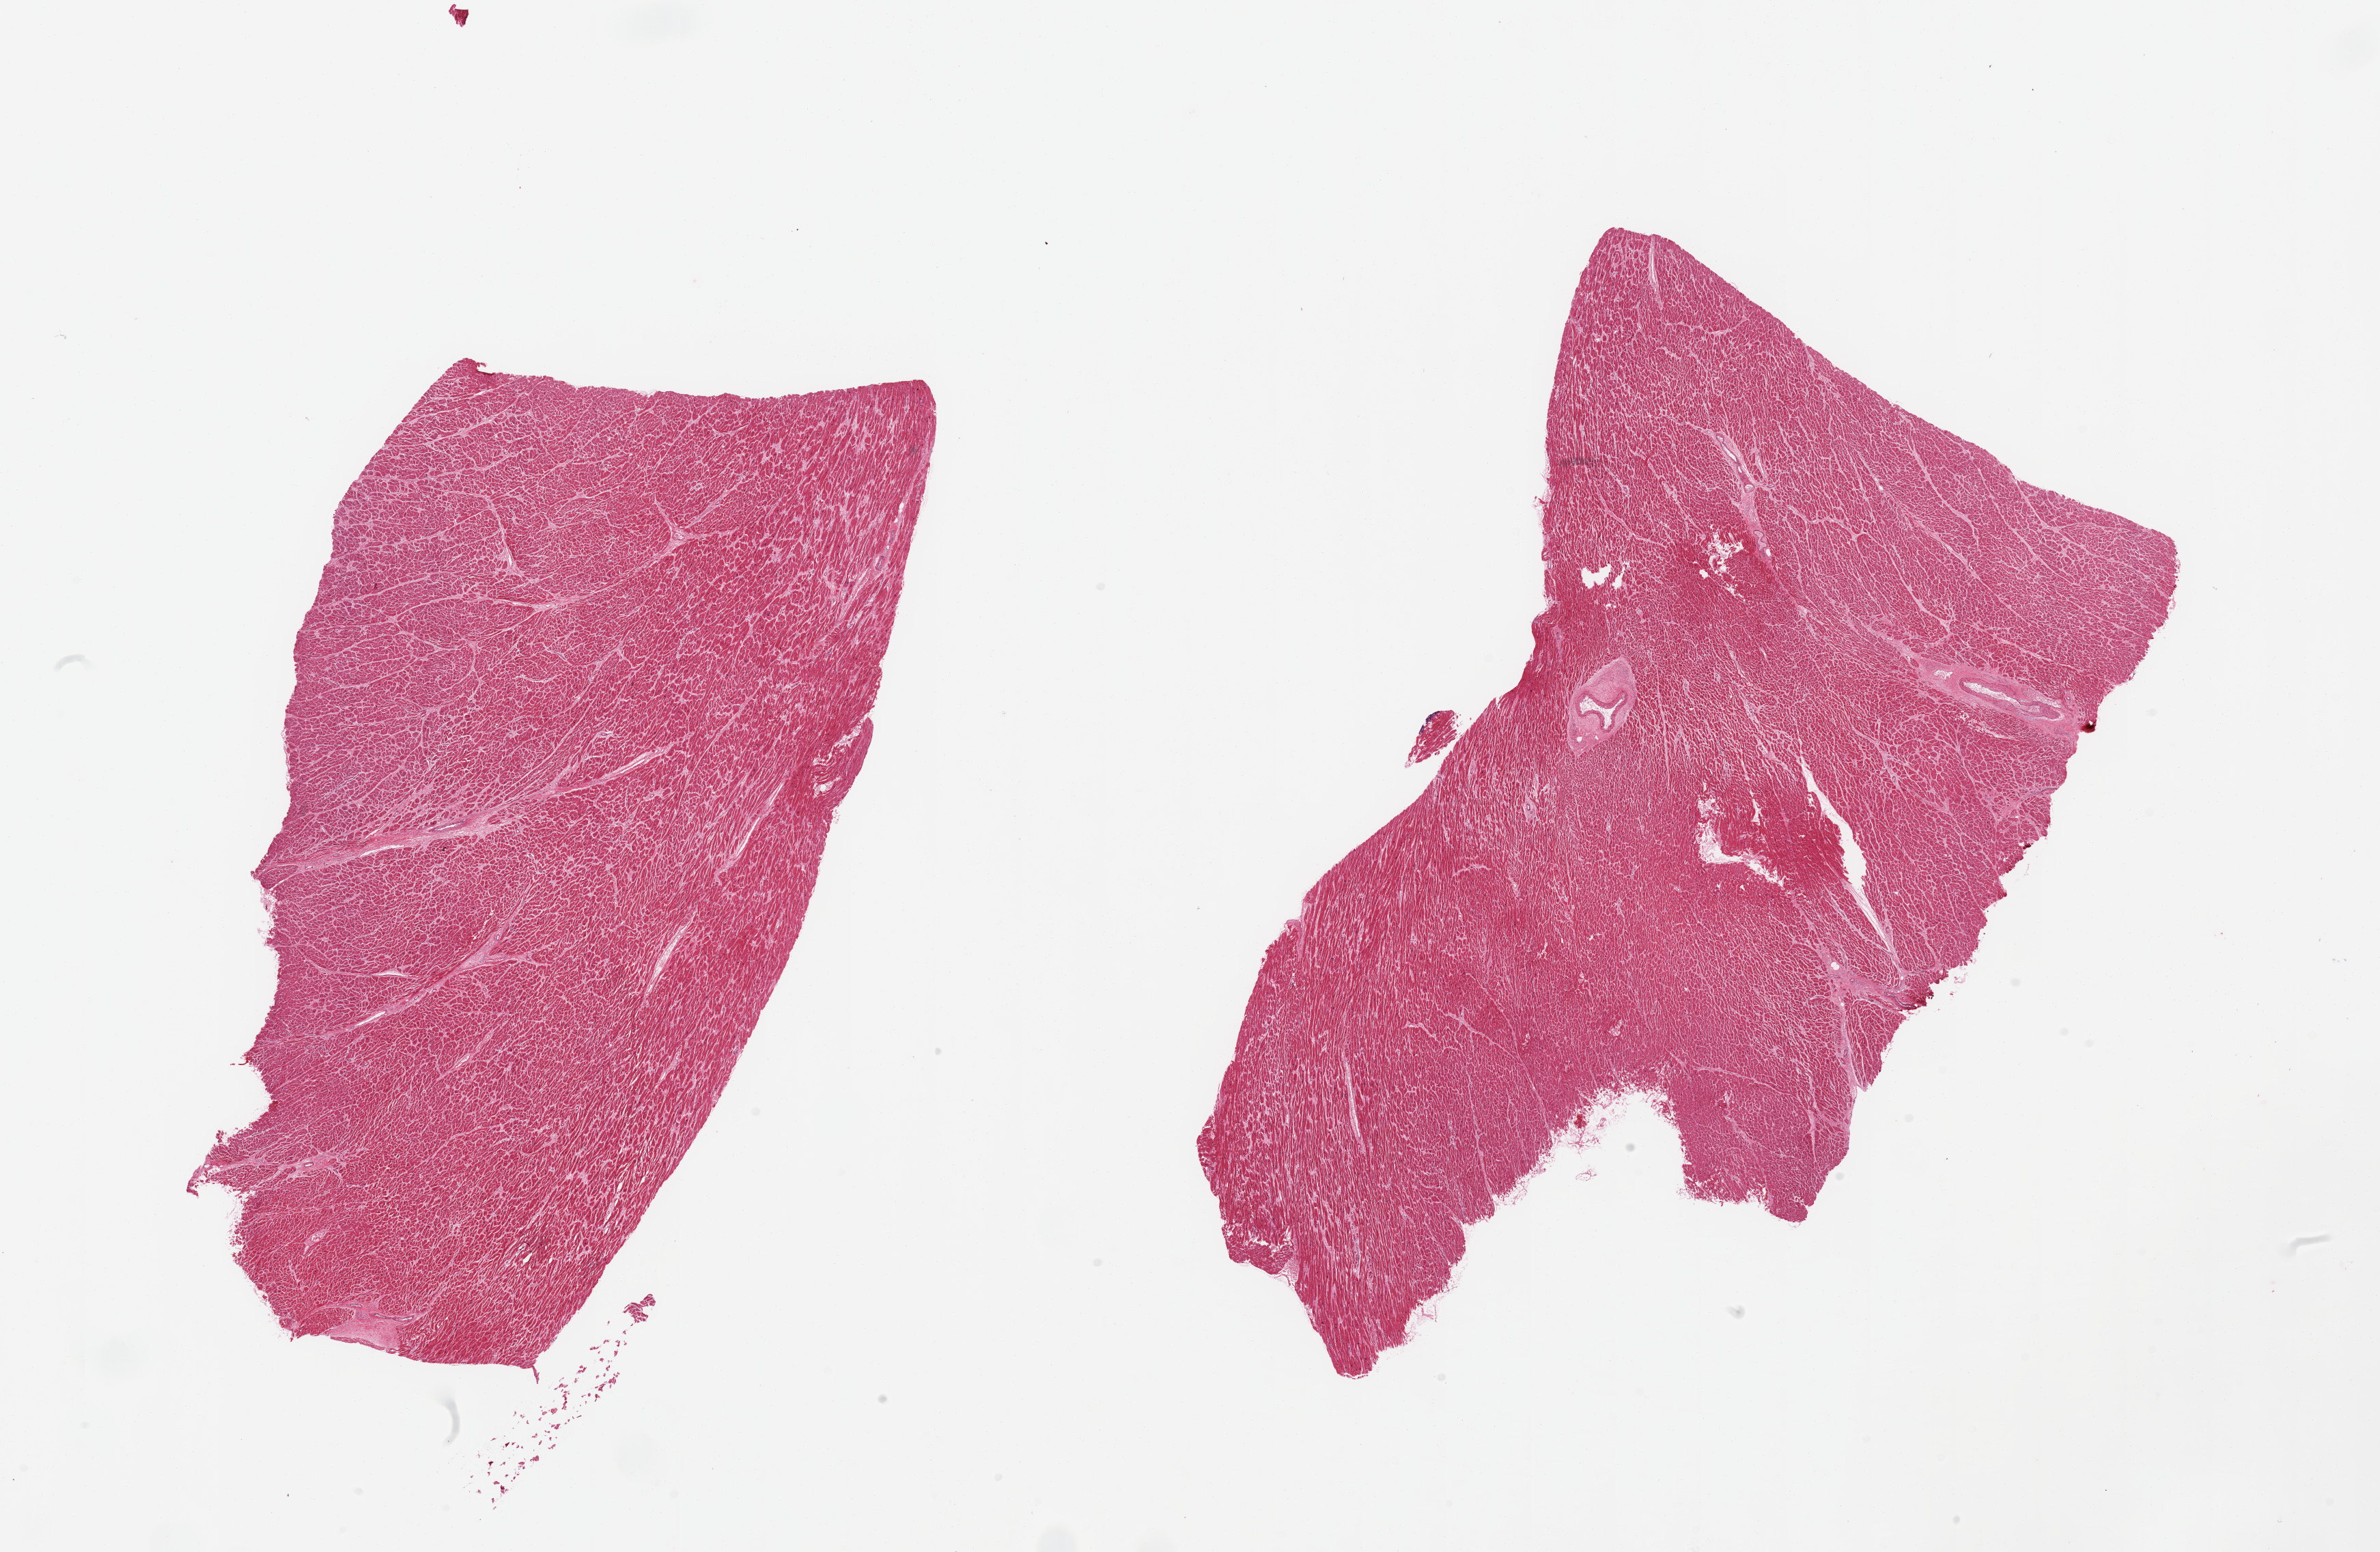
H&E whole-slide image — whole scanned area (about 27.6 x 18.0 mm, acquisition: 20x scan) shown as a low-resolution overview. PAXgene-fixed, paraffin-embedded tissue. Sampled site (target tissue): heart. Tissue donor sample. Male donor.
Reviewer comment on this tissue sample: 2 pieces; no acute changes; enlarged nuclei; slight increase in interstitial fibrous tissue.